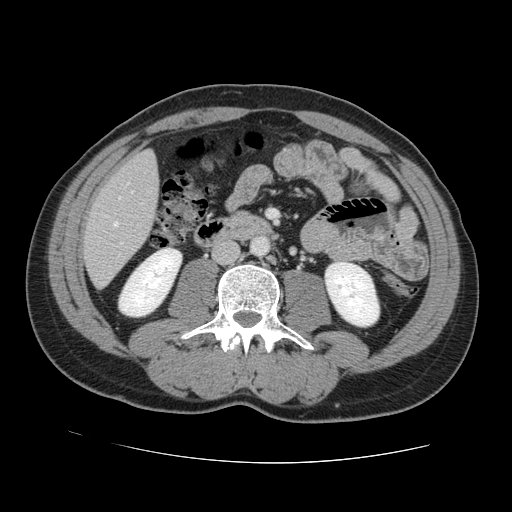
Contrast-enhanced abdominal CT, one axial slice; slice 33 of 131 in the series (ordered by position); 120 kVp; intravenous contrast given; soft-tissue window (W 400 / L 40 HU); 2.5 mm slice thickness; 512 × 512 image matrix, field of view 380 × 380 mm. Male patient, age 40 years. Case-level facts recorded for this patient, not image findings: diagnosis: colorectal cancer liver metastases, imaged before liver resection; multiple liver metastases: yes; largest metastasis: 2.9 cm; disease in both lobes: yes.
Structures marked on this image (manually delineated by an expert):
- hepatic veins: bounding box (x1, y1, x2, y2) in pixels: (113, 183, 128, 226)
- liver: (84, 152, 159, 286)
- planned liver remnant (the part of the liver to remain after resection): (146, 153, 152, 159)